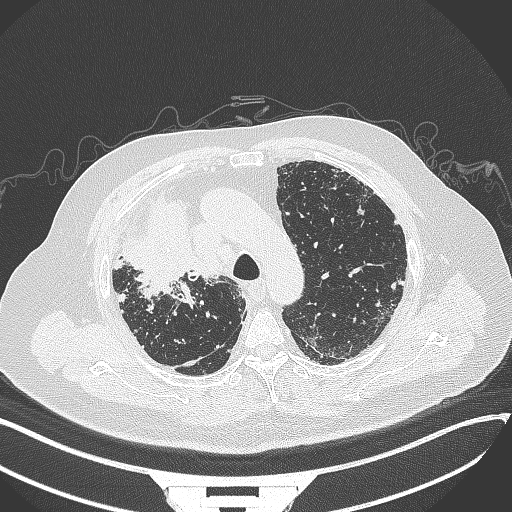
Chest CT, one axial slice. Slice 263 of 384 in the series (ordered by position). Reconstruction kernel B70f. 120 kVp. Lung window (W 1500 / L -600 HU). 1 mm slice thickness. 512 × 512 image matrix, field of view 400 × 400 mm. Male patient, age 69 years. Case-level facts recorded for this patient, not image findings: clinical TNM (as recorded): T4 N3 M1.
Annotated regions visible in this slice (rectangle marked by the reading radiologist):
- lung tumour (recorded histology: adenocarcinoma): bounding box [x1, y1, x2, y2] px = [121, 187, 218, 298]